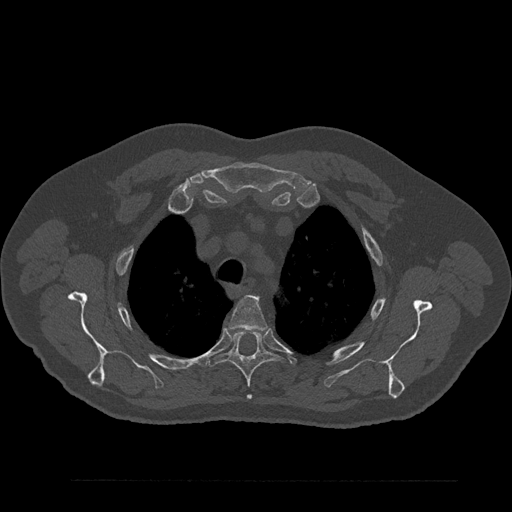
CT including the spine, one axial slice; position 655 of 797 along the scan axis; reconstruction kernel Br40s/3; 120 kVp; bone window (W 1800 / L 400 HU); 0.5 mm slice thickness; 512 × 512 image matrix, field of view 430 × 430 mm. Patient: male, 61 years. From the clinical record (not read from this slice): primary cancer: prostate.
Structures marked on this image (semi-automatically segmented with operator editing):
- T3 vertebra: bounding box [x1, y1, x2, y2] px = [229, 296, 266, 332]
- T4 vertebra: [205, 330, 284, 400]